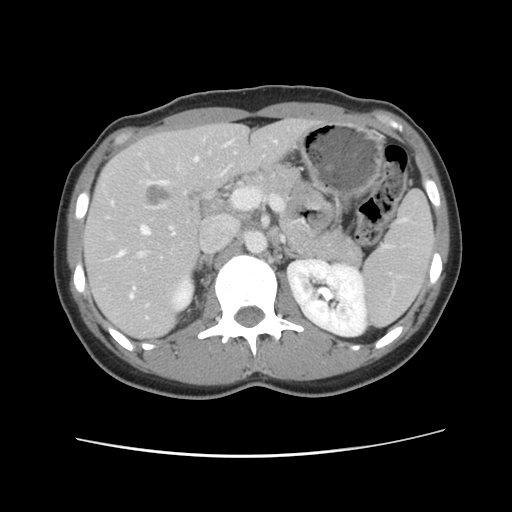
Contrast-enhanced abdominal CT, one axial slice. Slice 59 of 134 in the series (ordered by position). 120 kVp. Soft-tissue window (W 400 / L 40 HU). 512 × 512 image matrix, field of view 339 × 339 mm. Female patient, age 33 years. From the clinical record (not read from this slice): diagnosis: colorectal cancer liver metastases, imaged before liver resection; multiple liver metastases: yes; largest metastasis: 4.5 cm; disease in both lobes: yes.
Outlined on this slice (manually delineated by an expert):
- hepatic veins: bounding box [x1, y1, x2, y2] px = [112, 156, 199, 299]
- liver: [86, 120, 316, 338]
- planned liver remnant (the part of the liver to remain after resection): [86, 120, 316, 338]
- portal vein (with intrahepatic branches): [136, 225, 176, 258]
- liver metastasis: [143, 182, 179, 210]